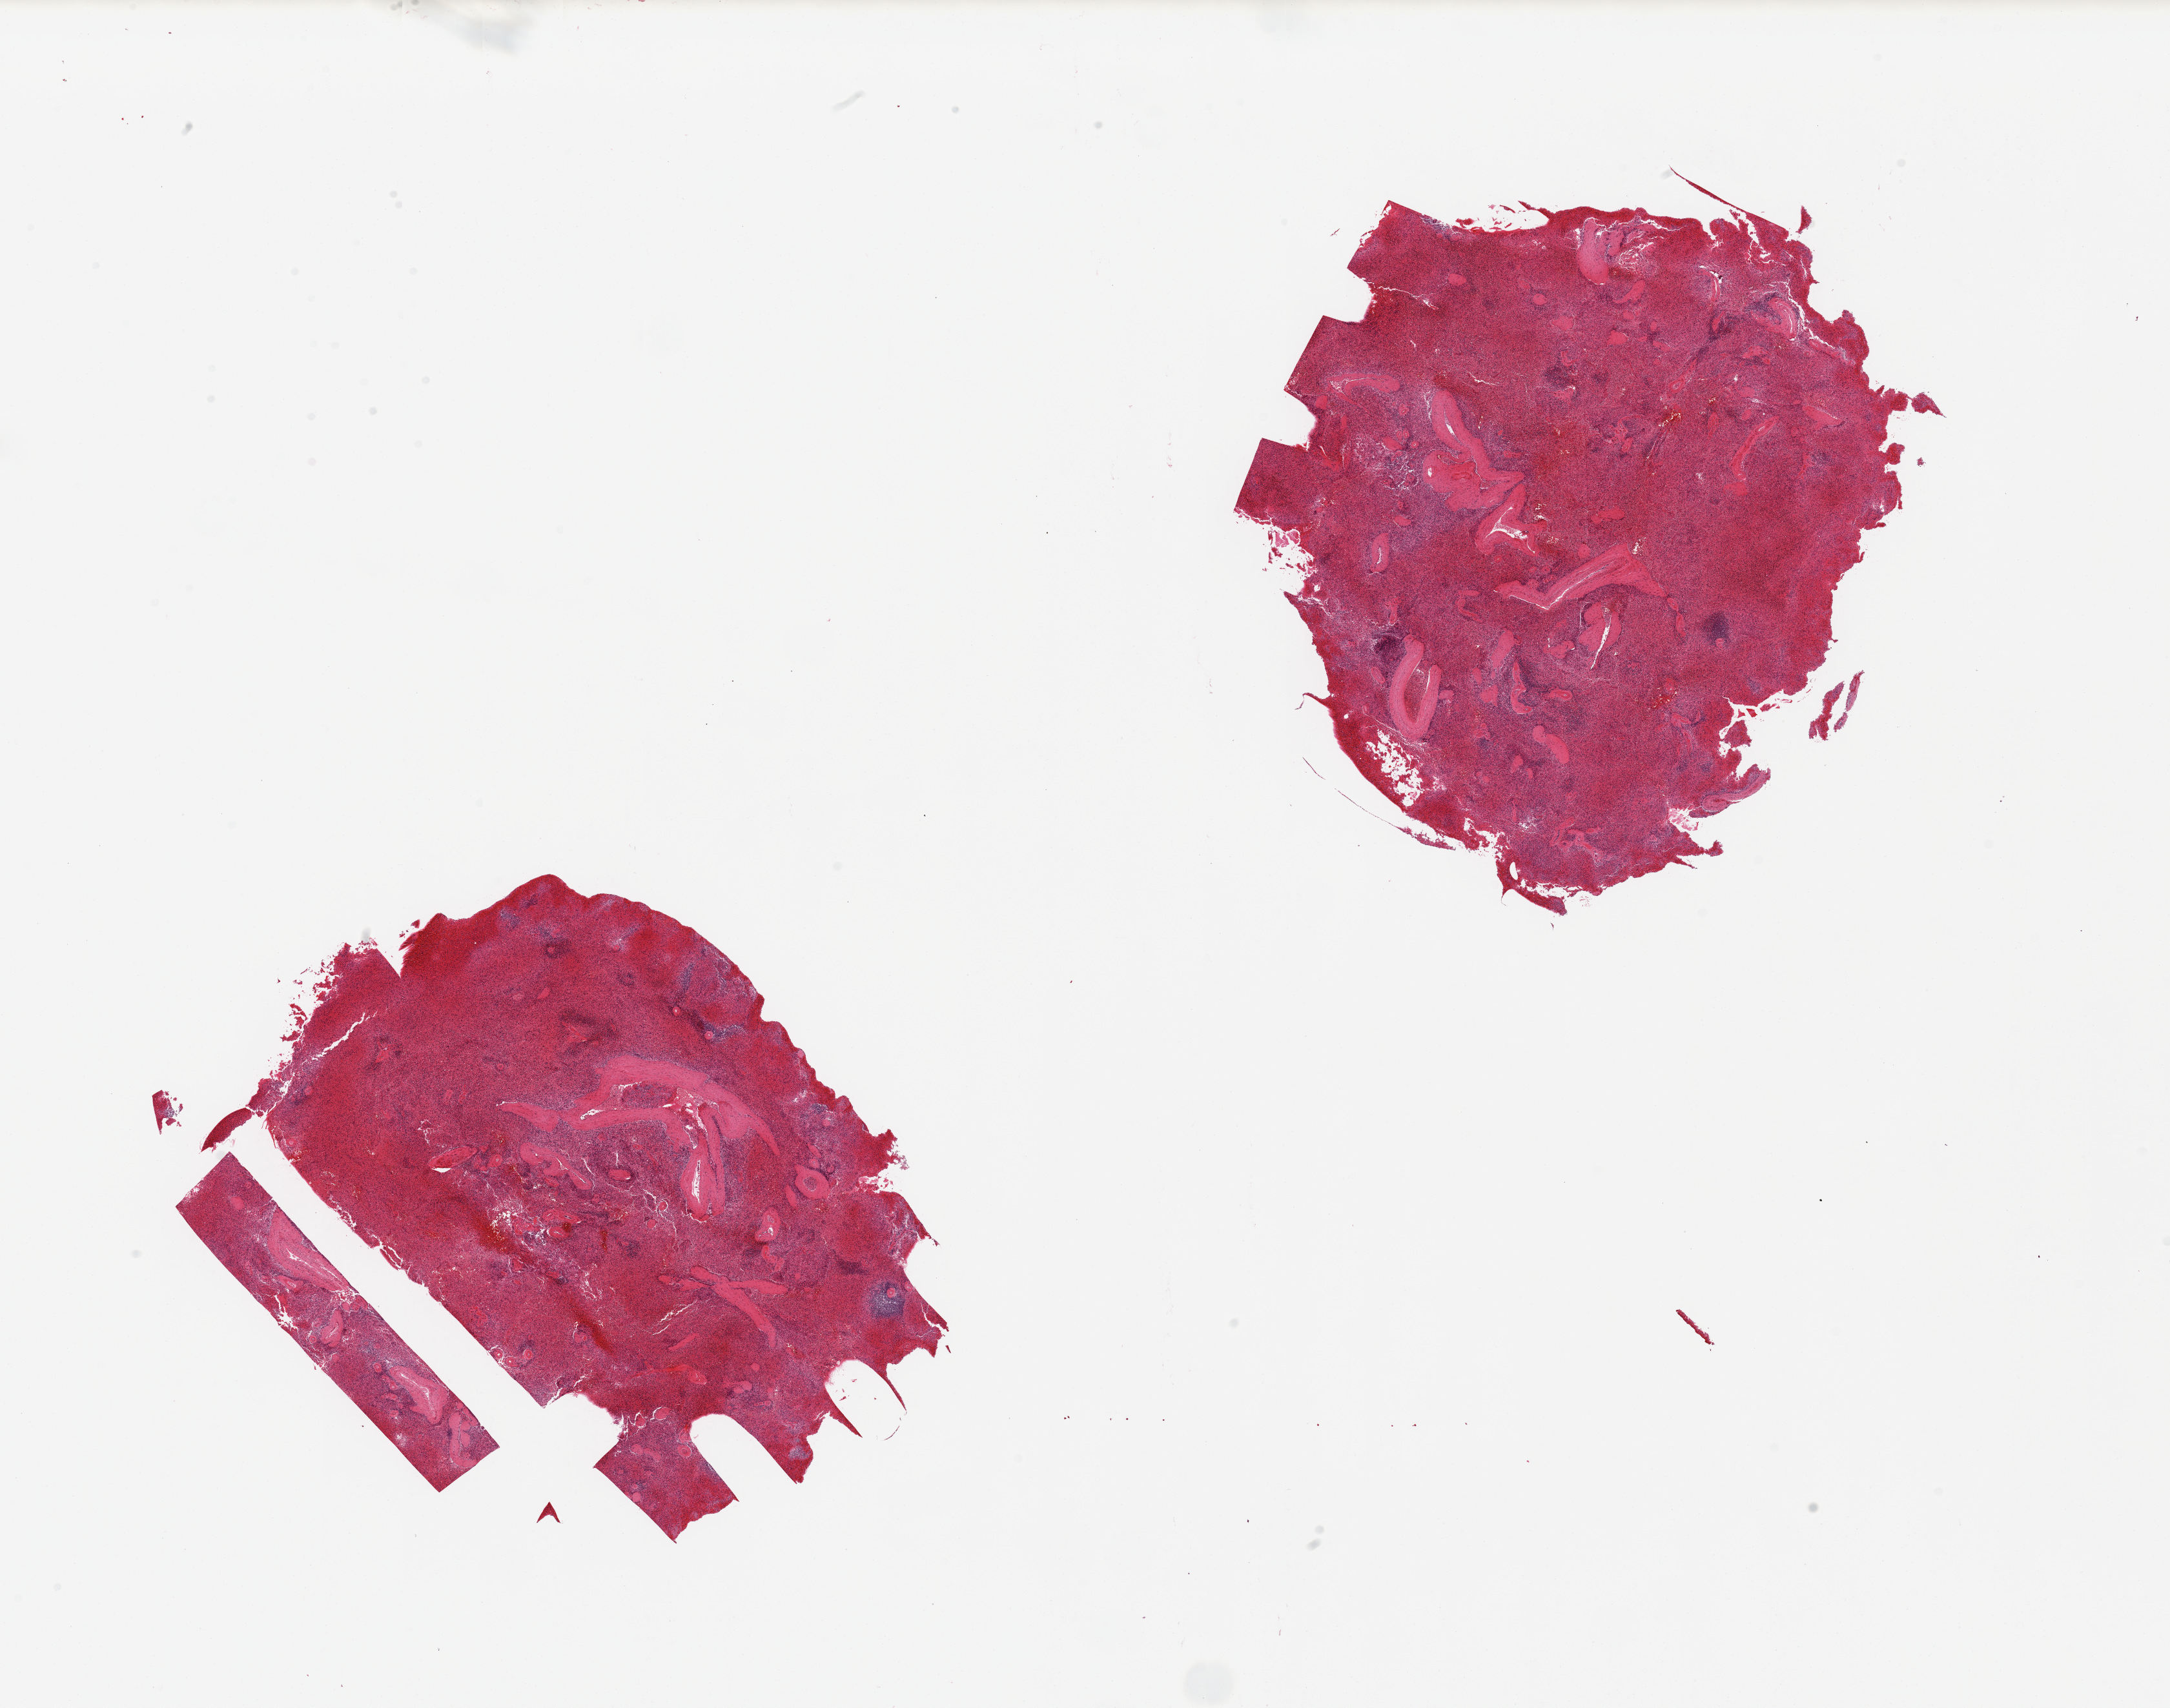
Hematoxylin and eosin (H&E) whole-slide image — whole scanned area (about 26.6 x 20.9 mm) shown as a low-resolution overview, PAXgene-fixed, paraffin-embedded tissue, section of spleen (target tissue), donor tissue sample.
* review note (as recorded): 2 pieces